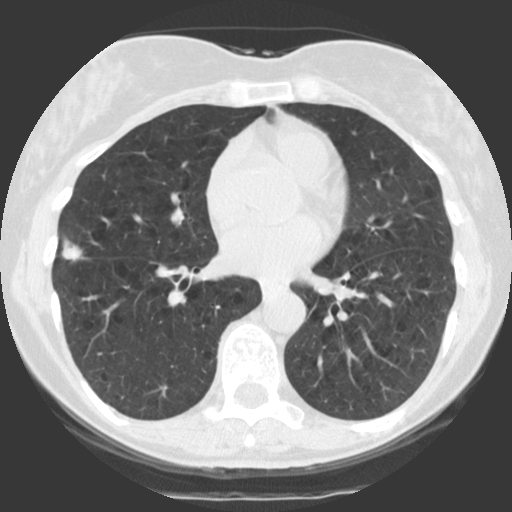
Low-dose screening chest CT, one axial slice; 140 kVp; lung window (W 1500 / L -600 HU); 512 × 512 image matrix.
Outlined on this slice (expert manual segmentation):
- lesion 1 (tumor, middle lobe of right lung): bounding box (x1, y1, x2, y2) in pixels: (62, 239, 85, 261)